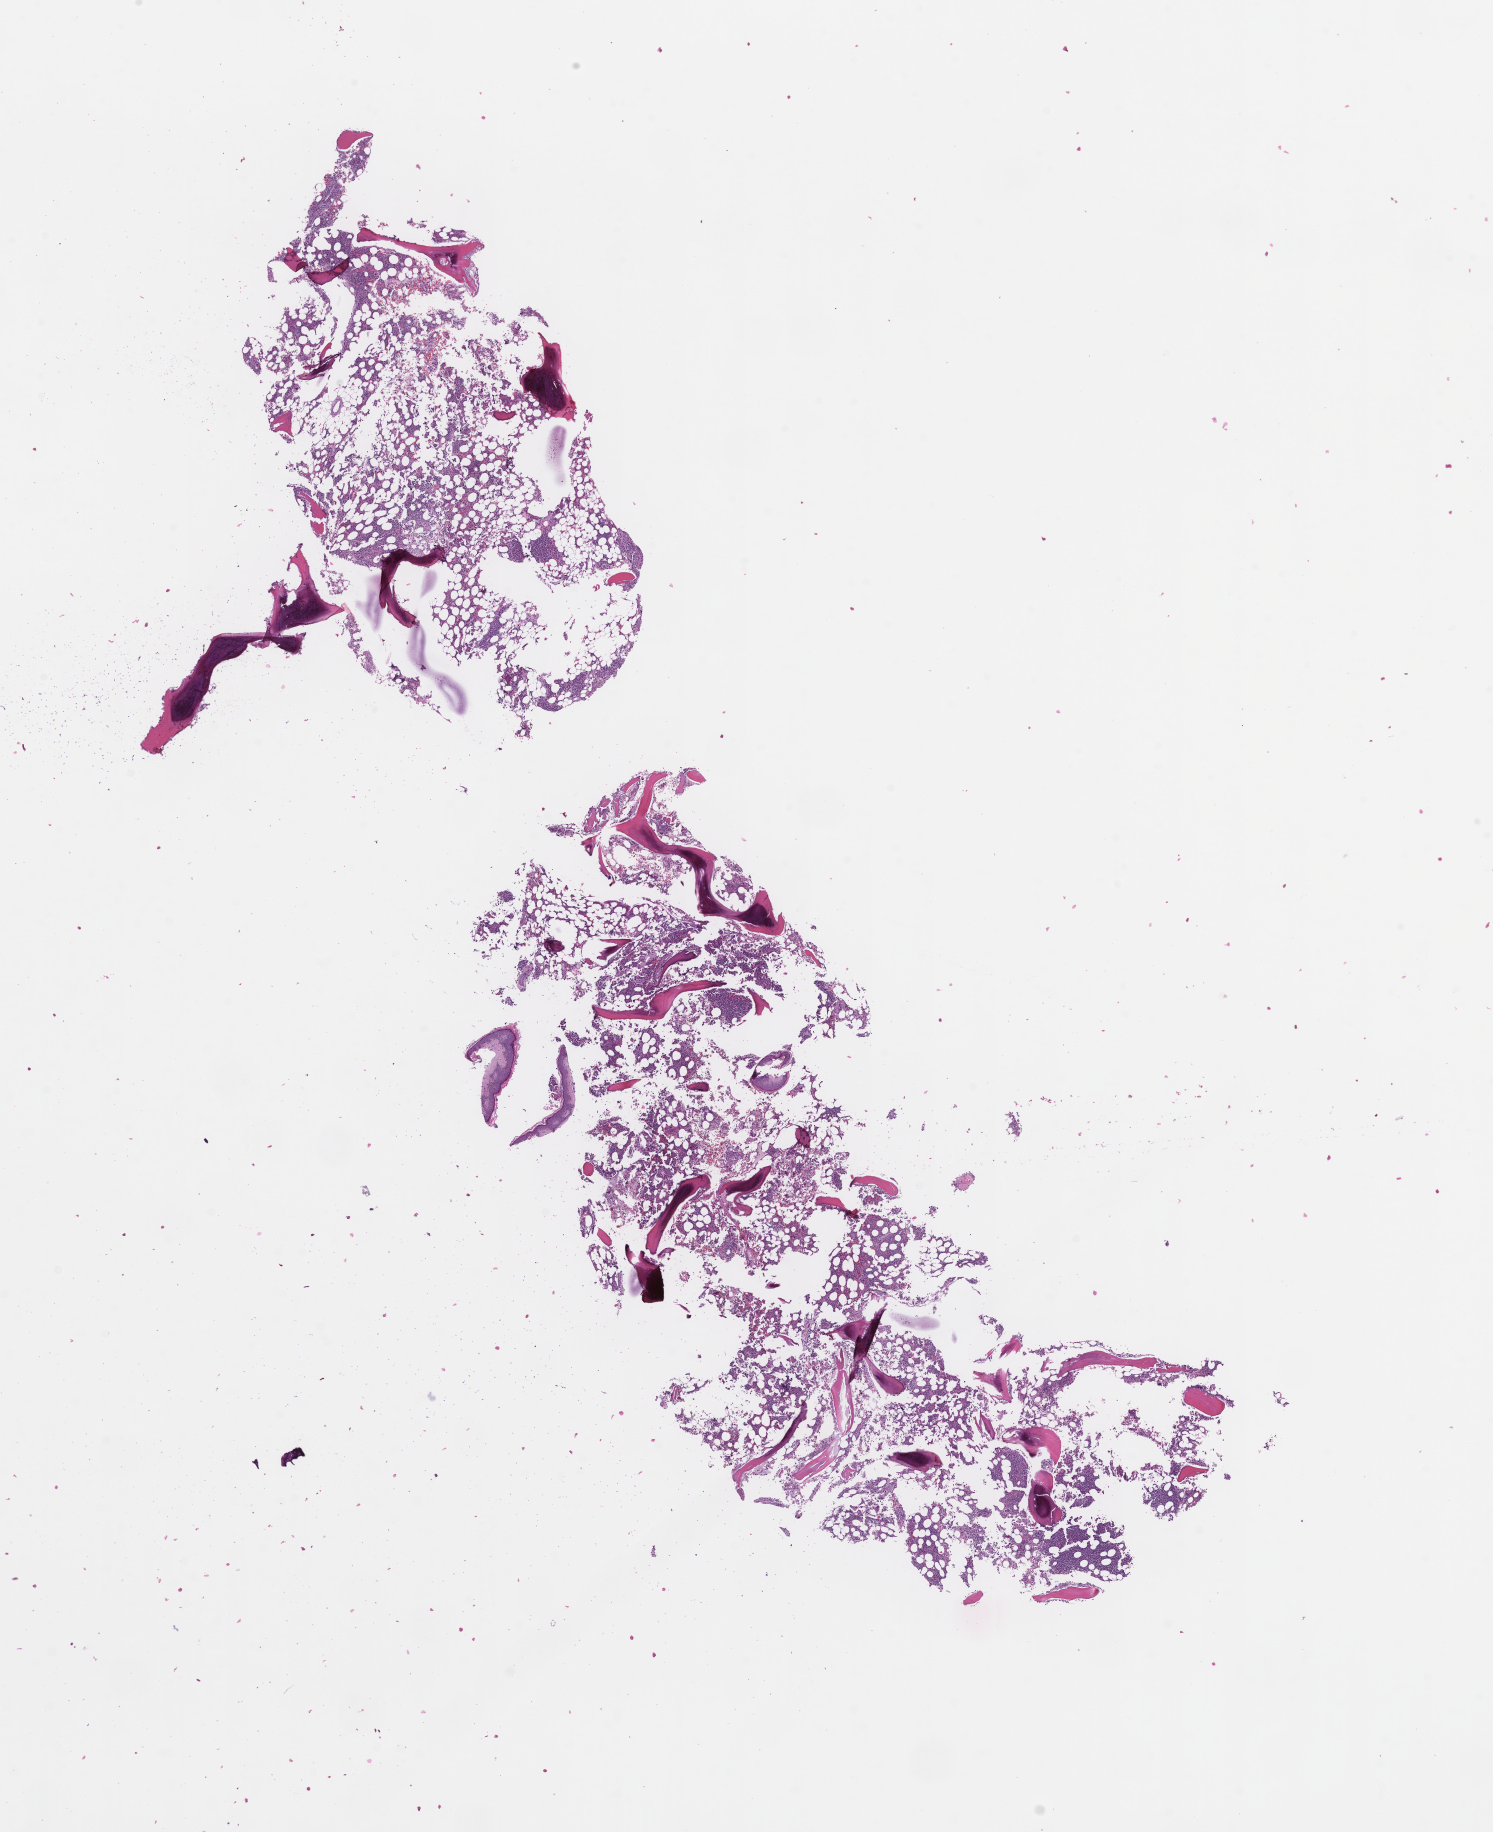
Whole-slide image, H&E stain, whole scanned area (about 12.1 x 14.8 mm) shown as a low-resolution overview; formalin-fixed paraffin-embedded section; tissue site: bone marrow; specimen time point: archival tissue. Male patient.
This section: primary tumour tissue. Diagnosis: Plasma Cell Myeloma.